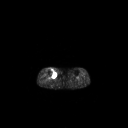
FDG PET of an extremity soft-tissue mass (from a PET/CT study), one axial slice. Position 145 of 267 along the scan axis. 3.27 mm slice thickness. 128 × 128 image matrix. Female patient, age 65 years. From the clinical record (not read from this slice): histological type: undifferentiated – high grade; grade: high; site of the primary tumour: right thigh.
Outlined on this slice (expert contour drawn on MRI and transferred to this co-registered scan by the dataset authors):
- gross tumour volume (mass): bounding box <51,69,57,77> (left, top, right, bottom; pixels)